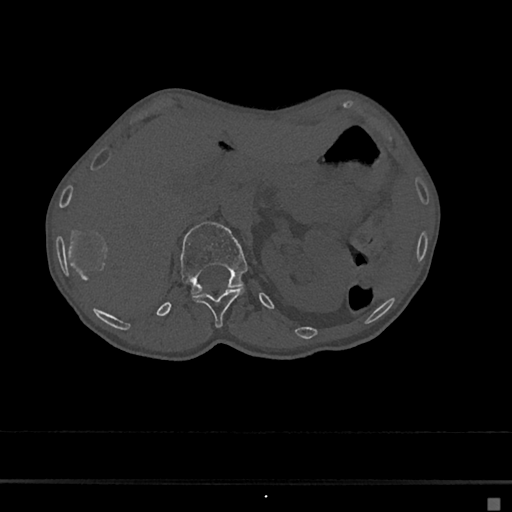
CT including the spine, one axial slice; slice 94 of 797 in the series (ordered by position); reconstruction kernel Br40s/3; 120 kVp; bone window (W 1800 / L 400 HU); 0.5 mm slice thickness; 512 × 512 image matrix, field of view 360 × 360 mm. Patient: female, 68 years. From the clinical record (not read from this slice): primary cancer: renal.
Annotated regions visible in this slice (semi-automatically segmented with operator editing):
- L1 vertebra: bounding box <180,222,248,295> (left, top, right, bottom; pixels)
- T12 vertebra: <192,288,244,328>